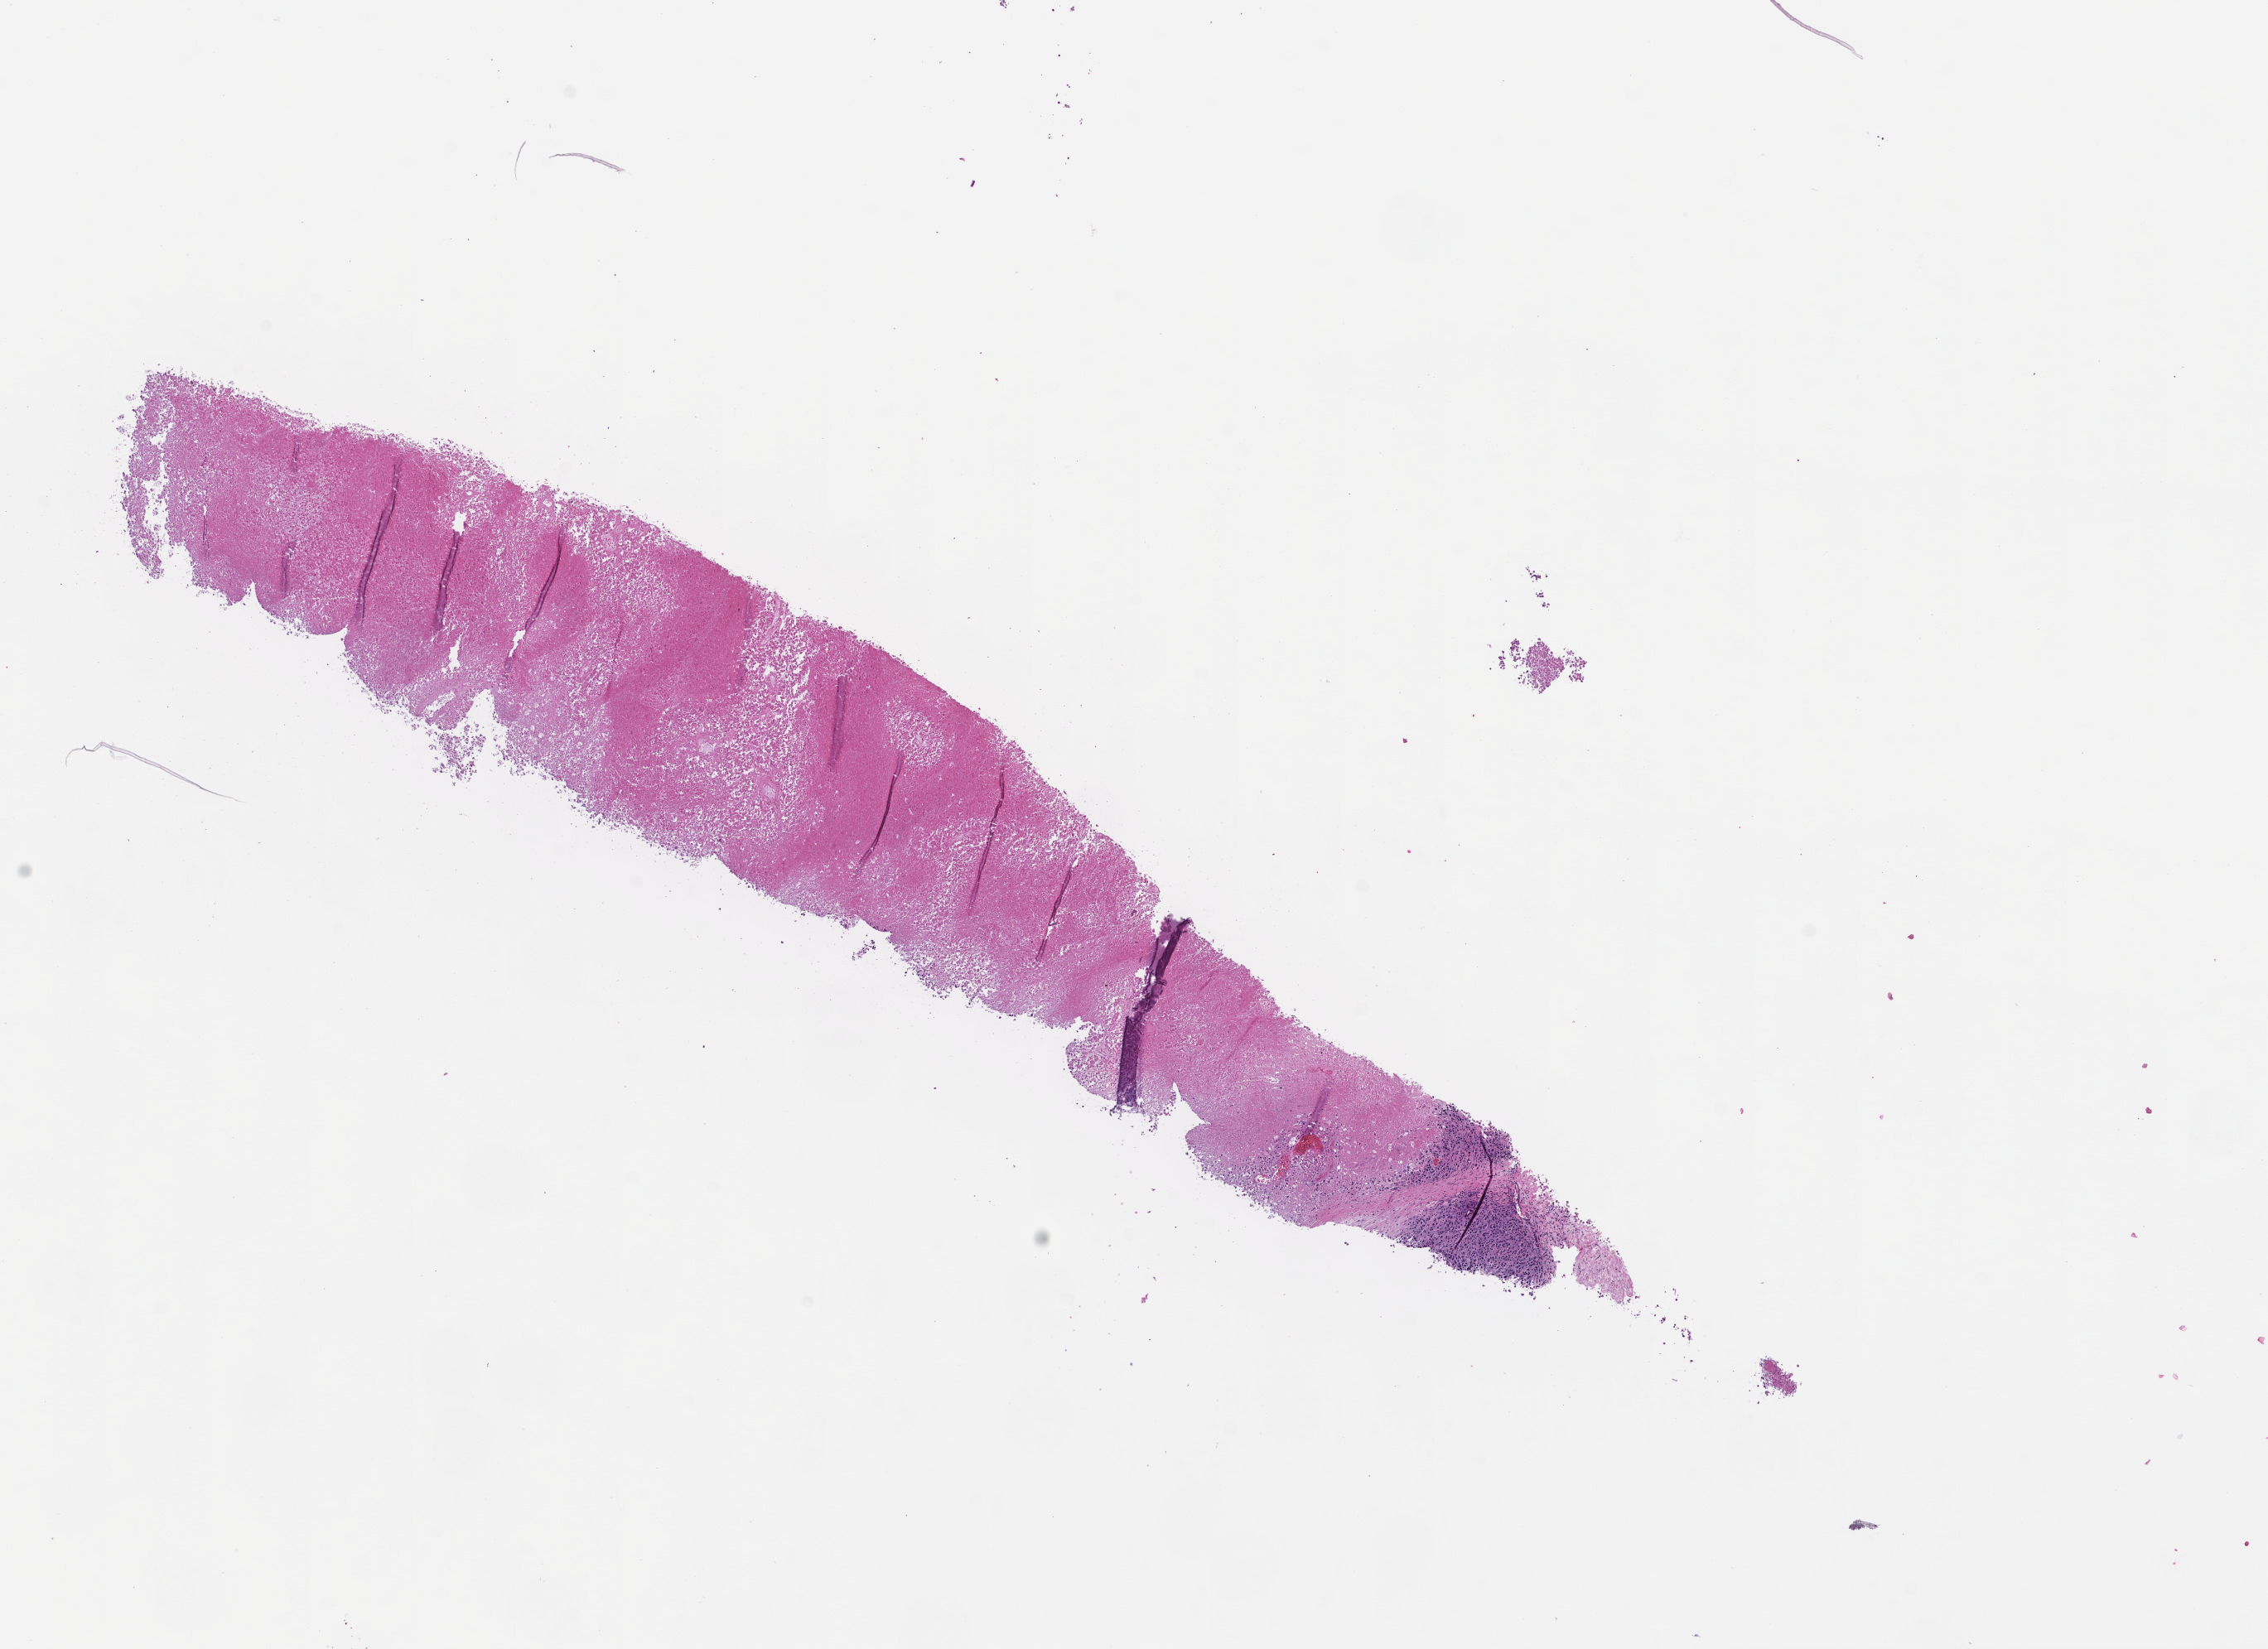
Digitized H&E-stained section — low-resolution overview of the scanned area, about 11.1 x 8.0 mm, formalin-fixed, paraffin-embedded (FFPE) tissue, collected at disease progression. Patient sex: female.
This section: metastatic tumor tissue. Patient diagnosis (primary): Melanoma.